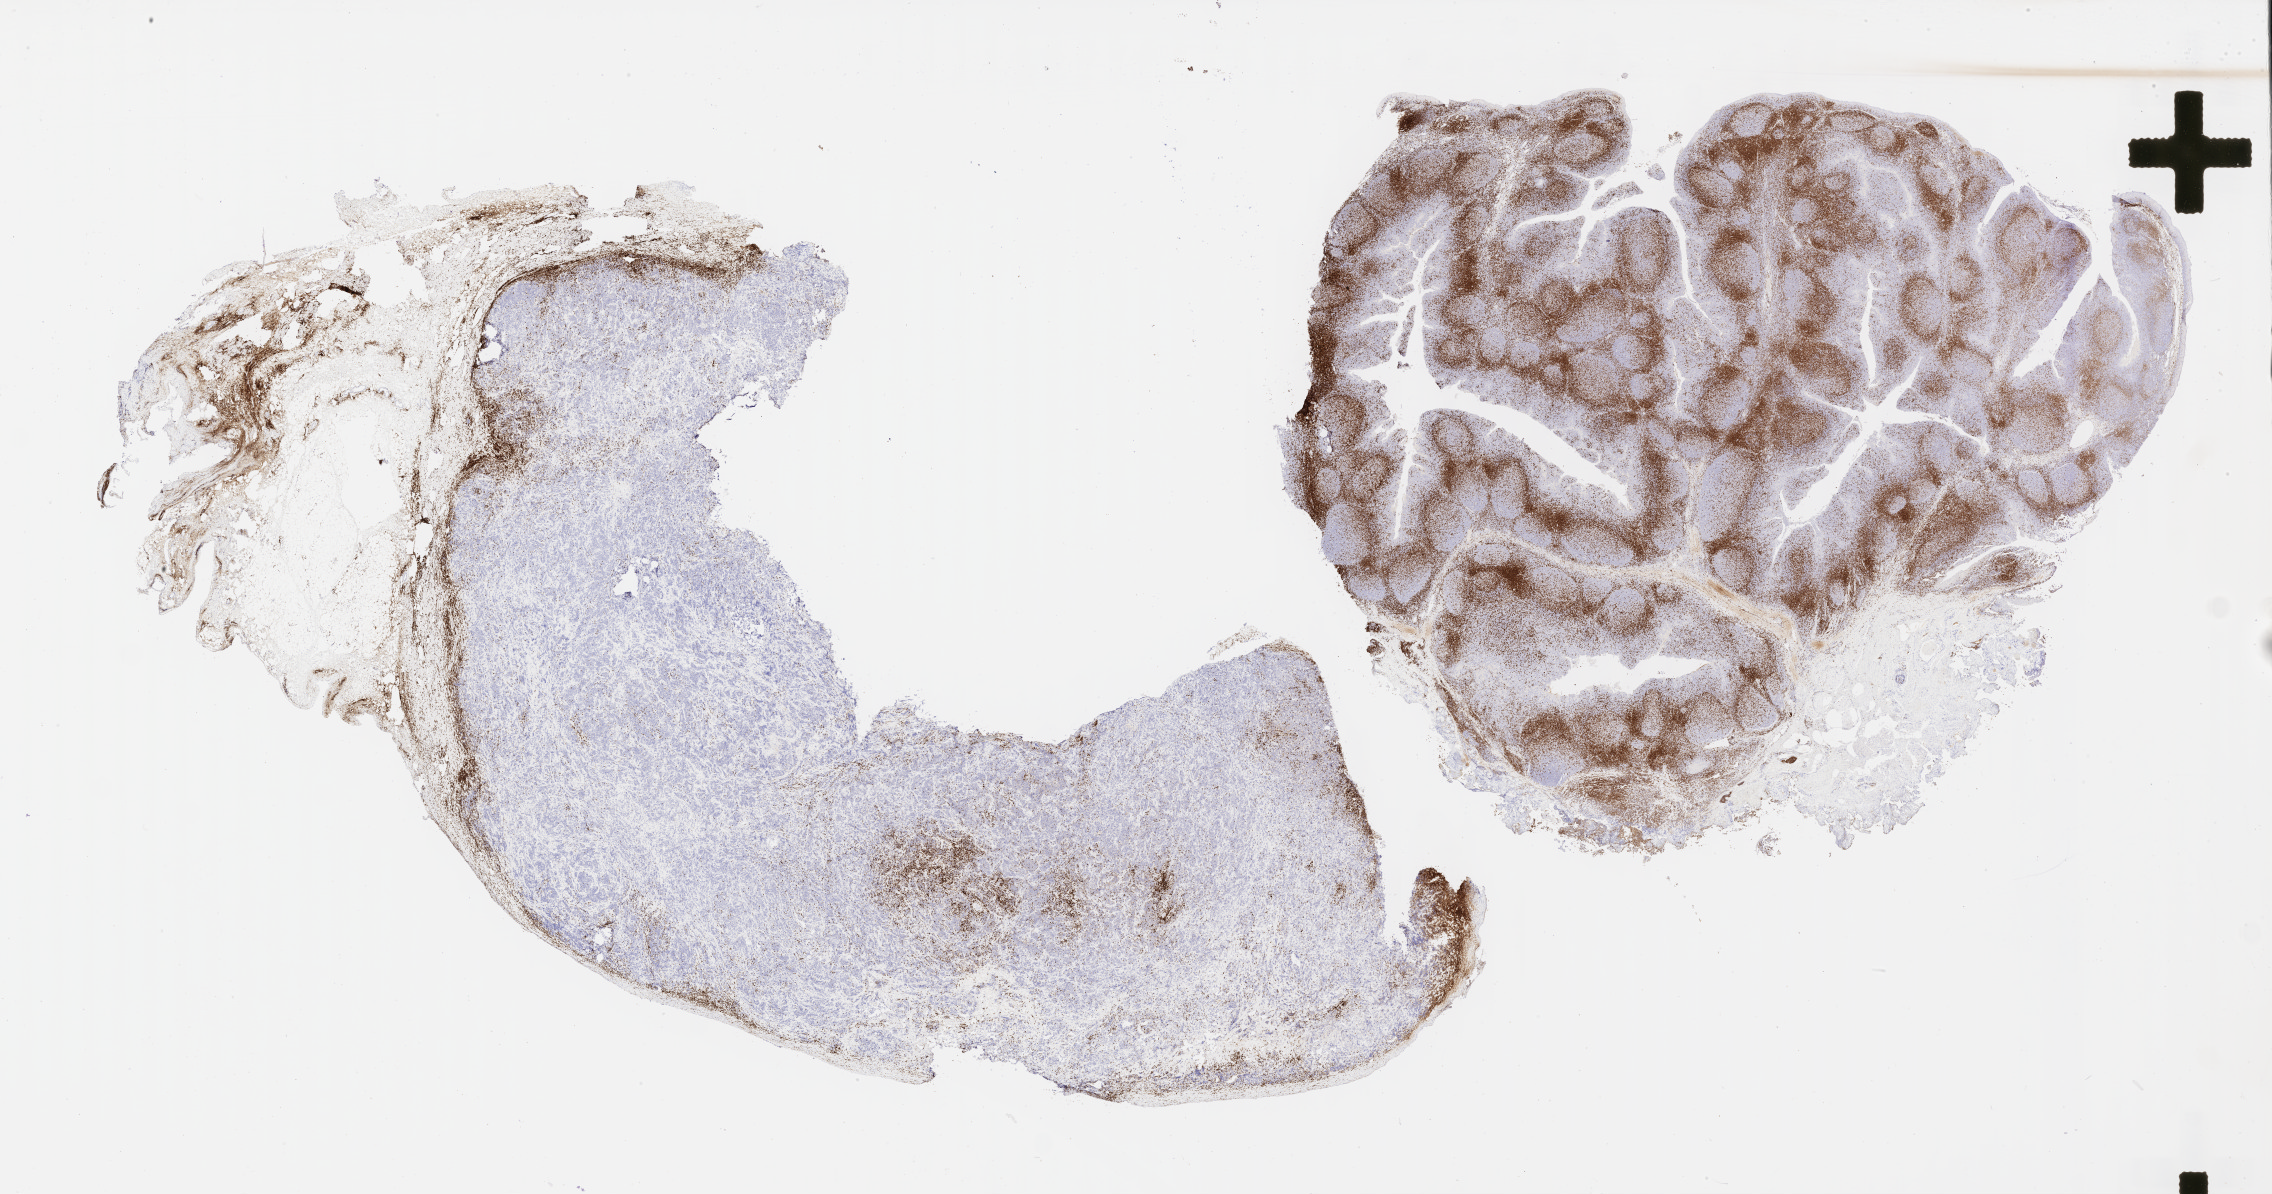
Immunohistochemistry (IHC) whole-slide image stained for CD3, shown as a low-resolution overview of the whole scanned area (about 36.7 x 19.3 mm); tumor tissue; anatomic site: bone. Male patient, age 48 years.
Histologic diagnosis: Diffuse large B-cell lymphoma, NOS.